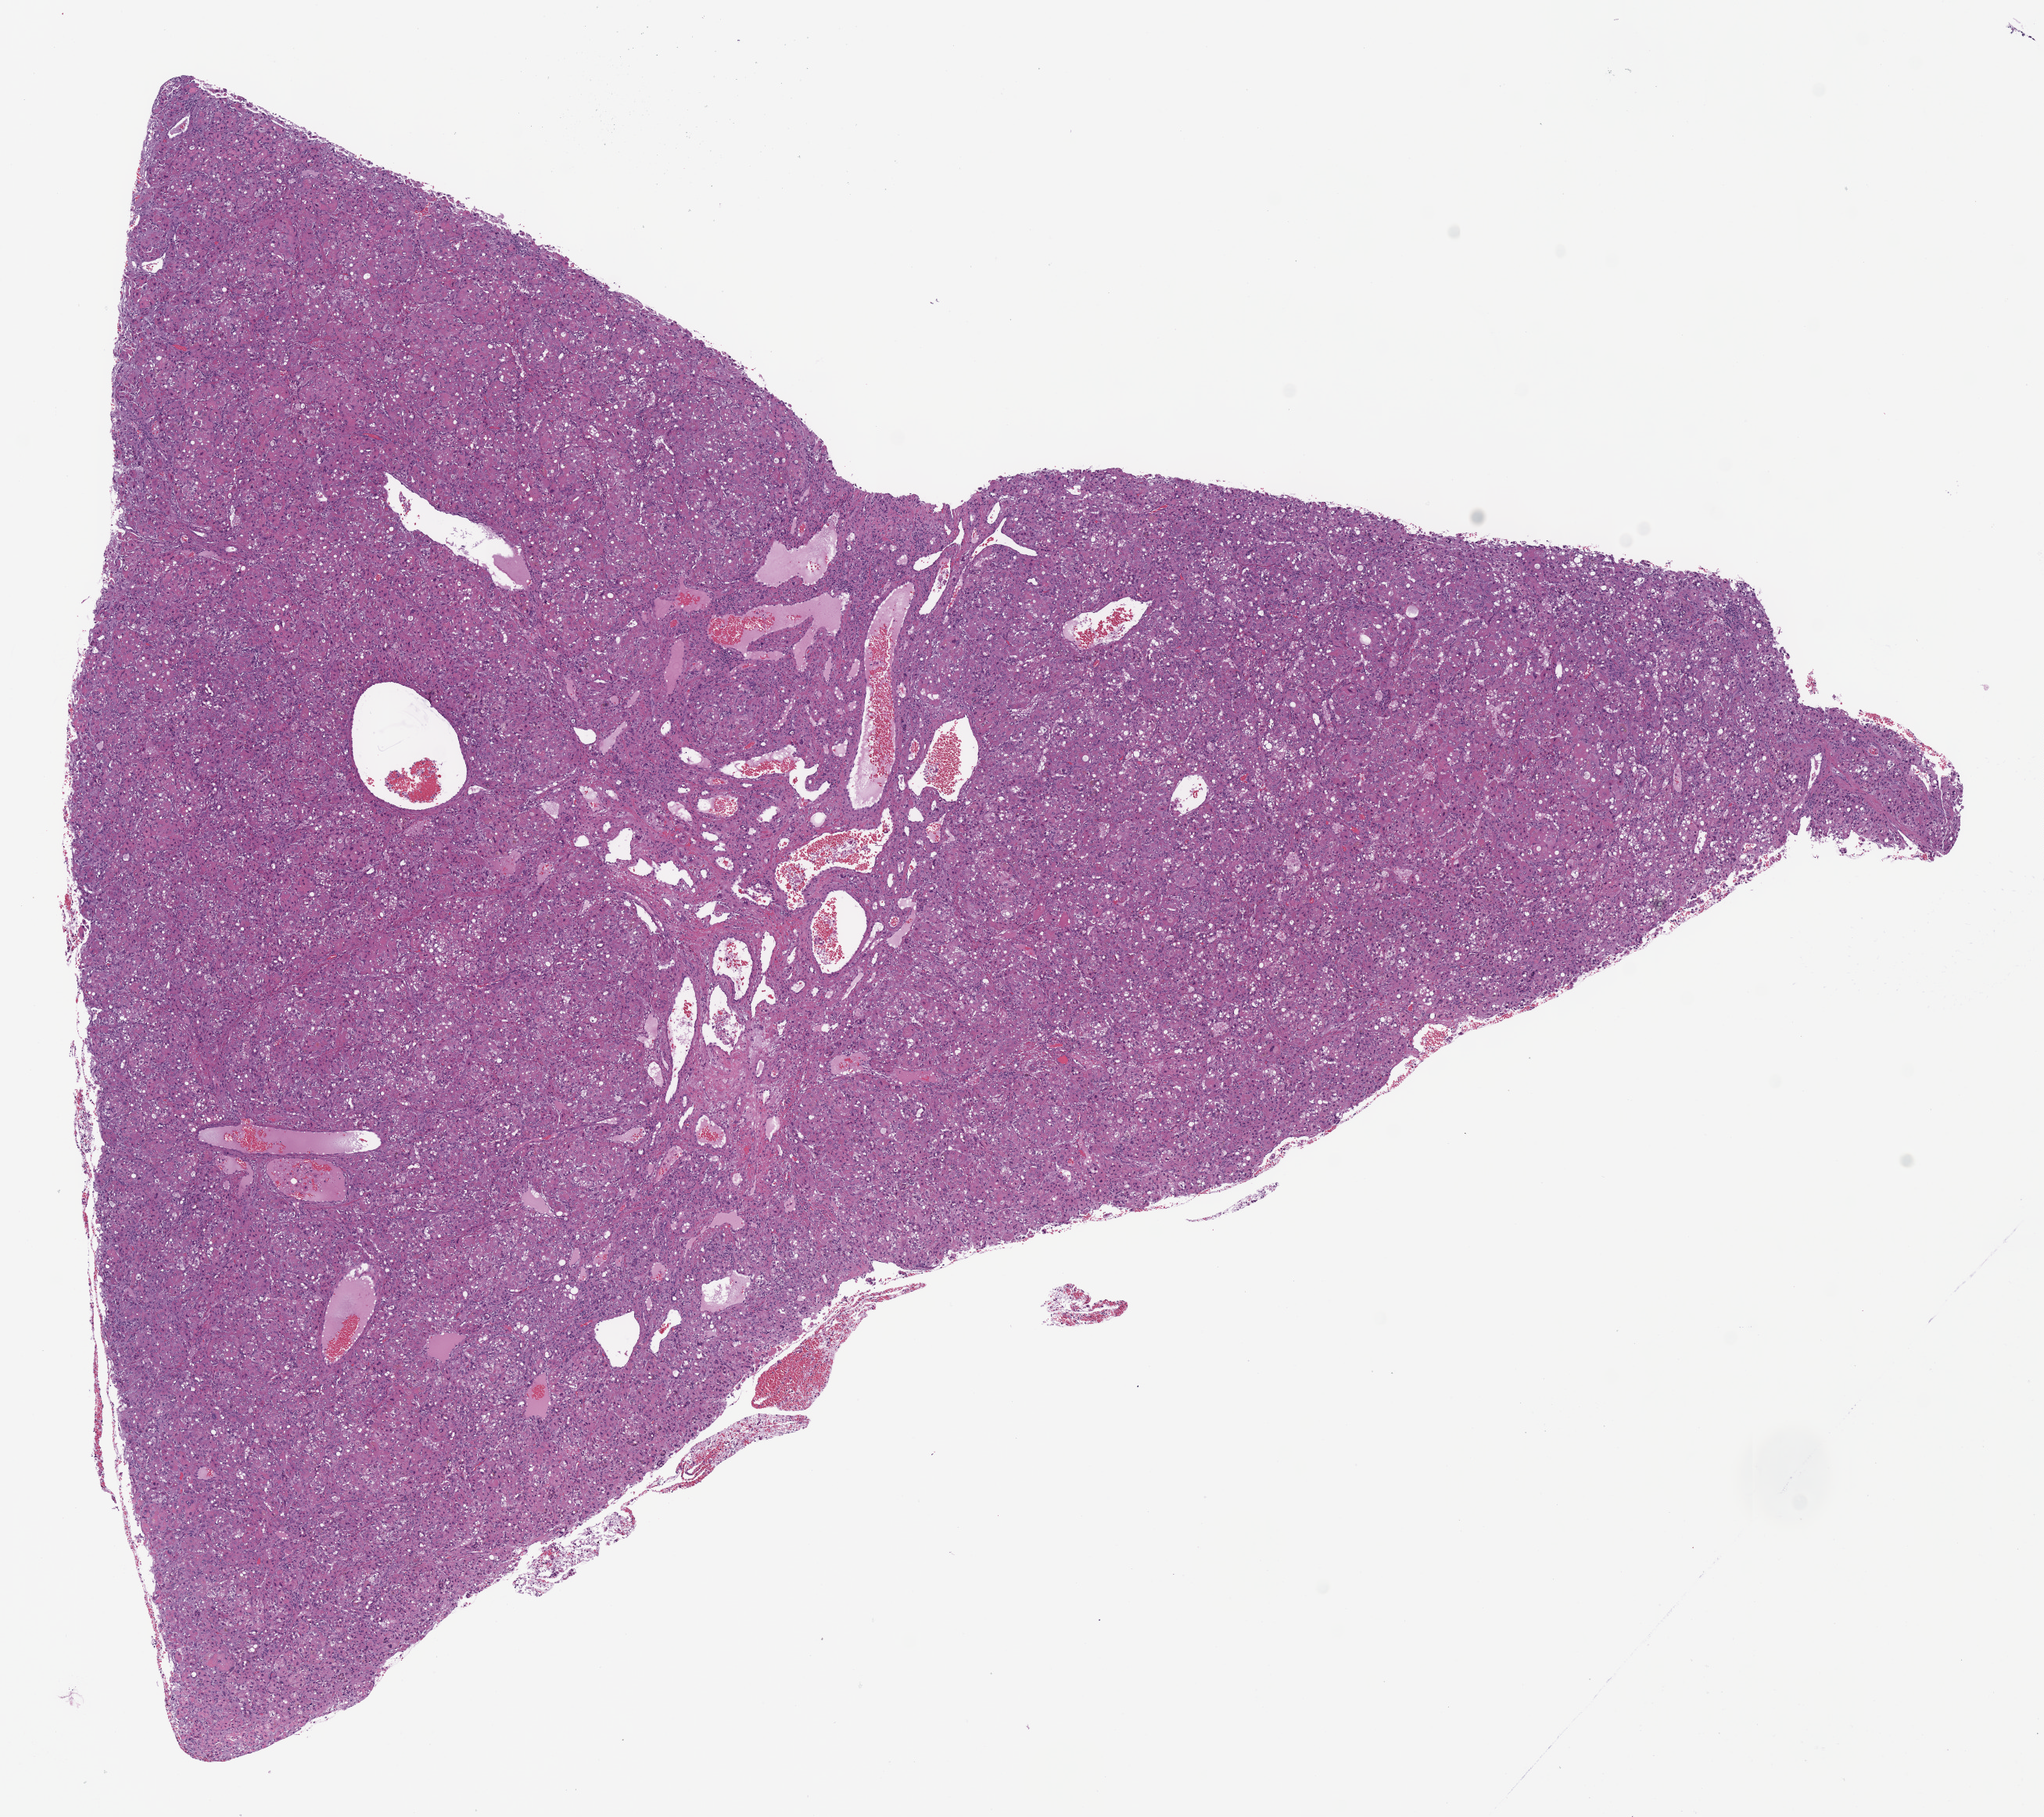
Hematoxylin and eosin (H&E) stained whole-slide image, low-resolution overview of the scanned area, about 10.3 x 9.1 mm (from a 40x scan). FFPE section. Primary tumour sample from the liver. Female, age 38 years at initial diagnosis. Histologic grade: G2 (moderately differentiated).
AJCC pathologic stage: I (7th edition). Histologic diagnosis: Hepatocellular carcinoma, NOS.